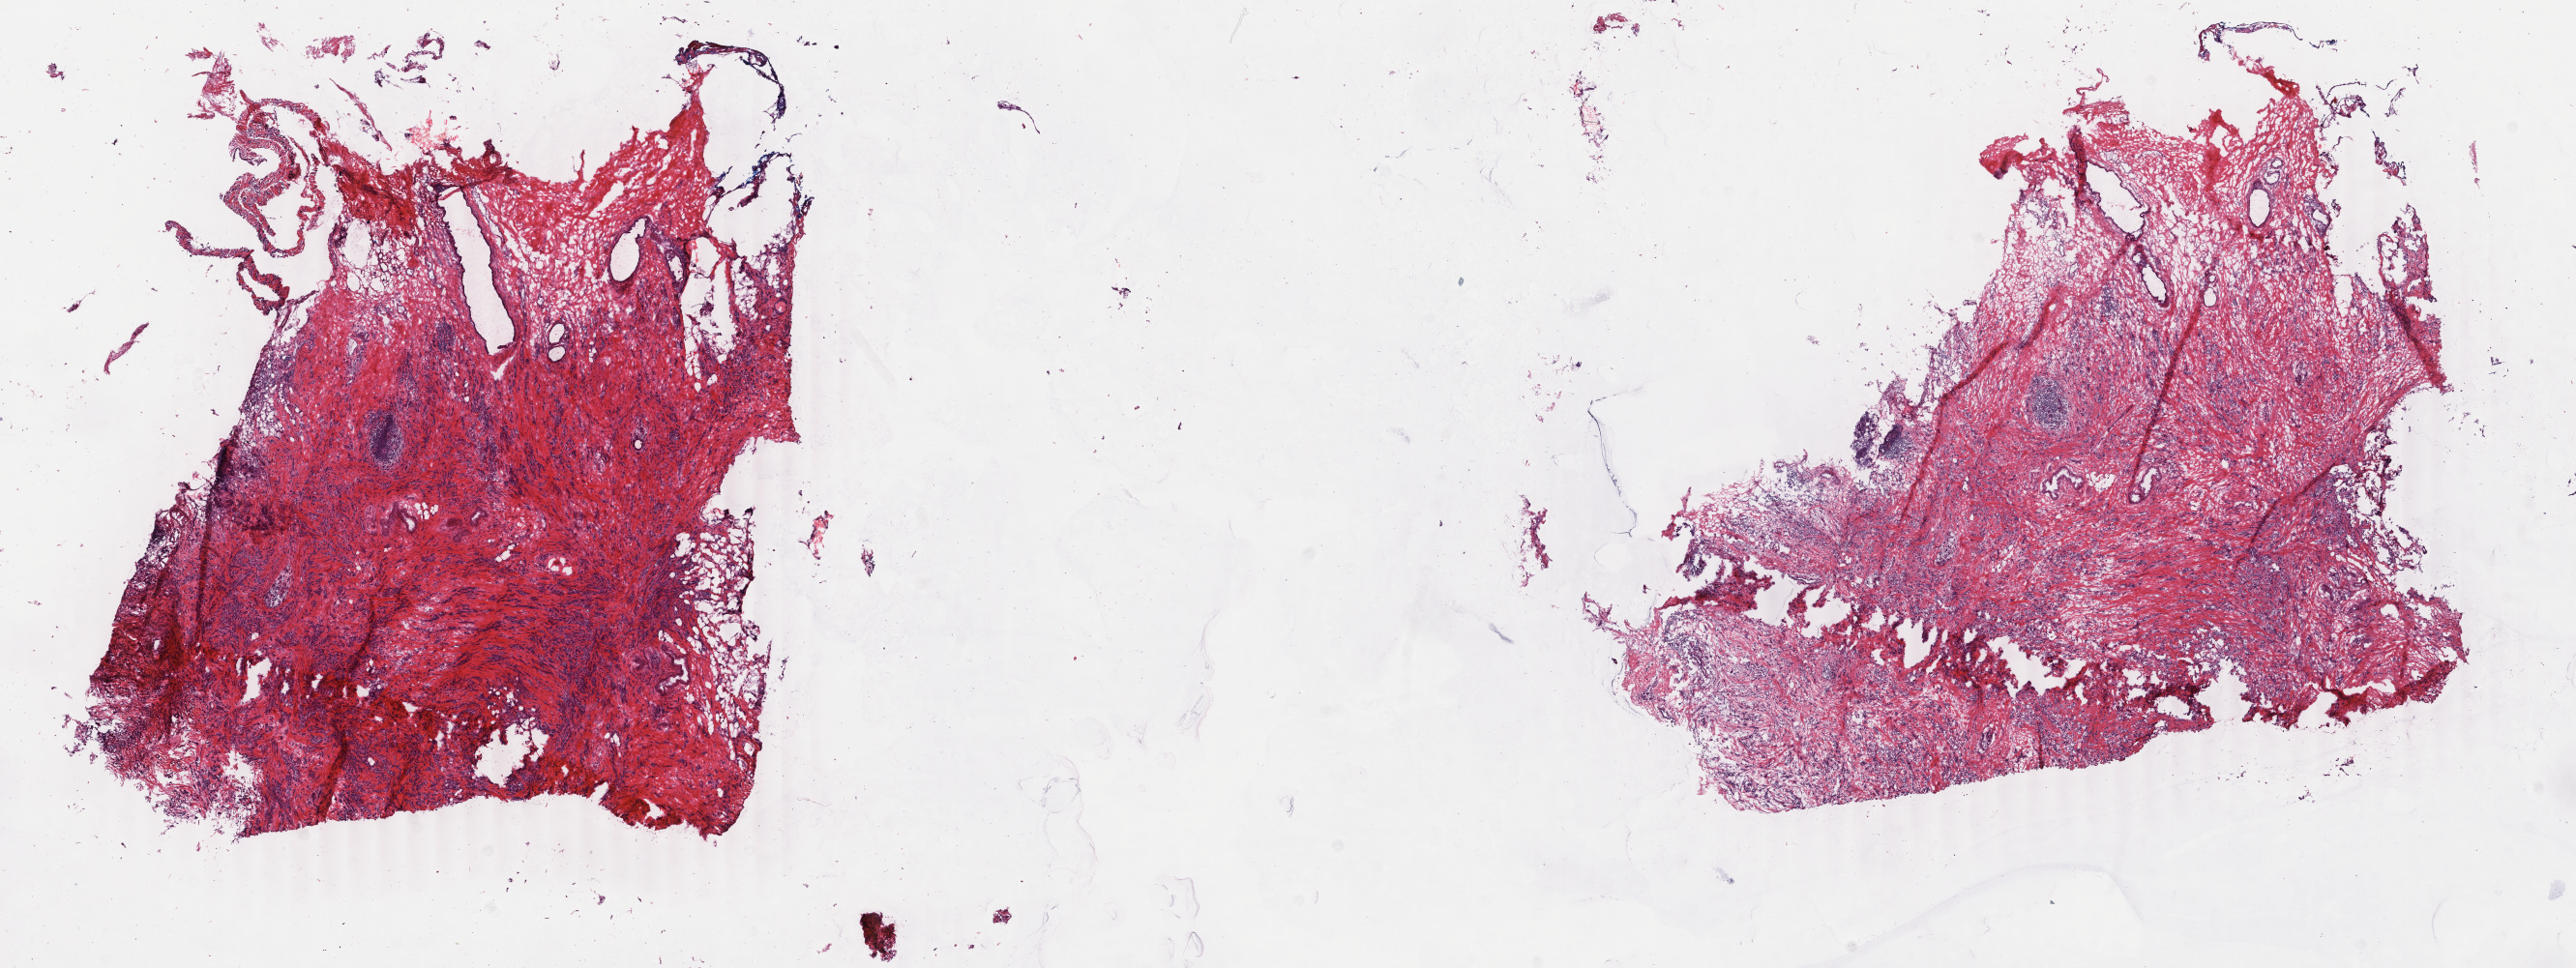
Whole-slide histology image, H&E-stained, low-resolution overview of the scanned area, about 21.2 x 8.0 mm, frozen section from the top of the tissue portion, breast, primary tumour sample. Female patient; age at initial diagnosis 61 years. Pathologist review of this section (percent, as recorded): tumour cells 75%, tumour nuclei 75%, normal cells 15%, stromal cells 10%, necrosis 0%. Infiltration values recorded for this section: lymphocyte infiltration 0%, monocyte infiltration 0%, neutrophil infiltration 0%.
AJCC pathologic stage: IIA. Lymph nodes positive (case pathology): 0 of 3 examined. Pathologic diagnosis: Lobular carcinoma, NOS.